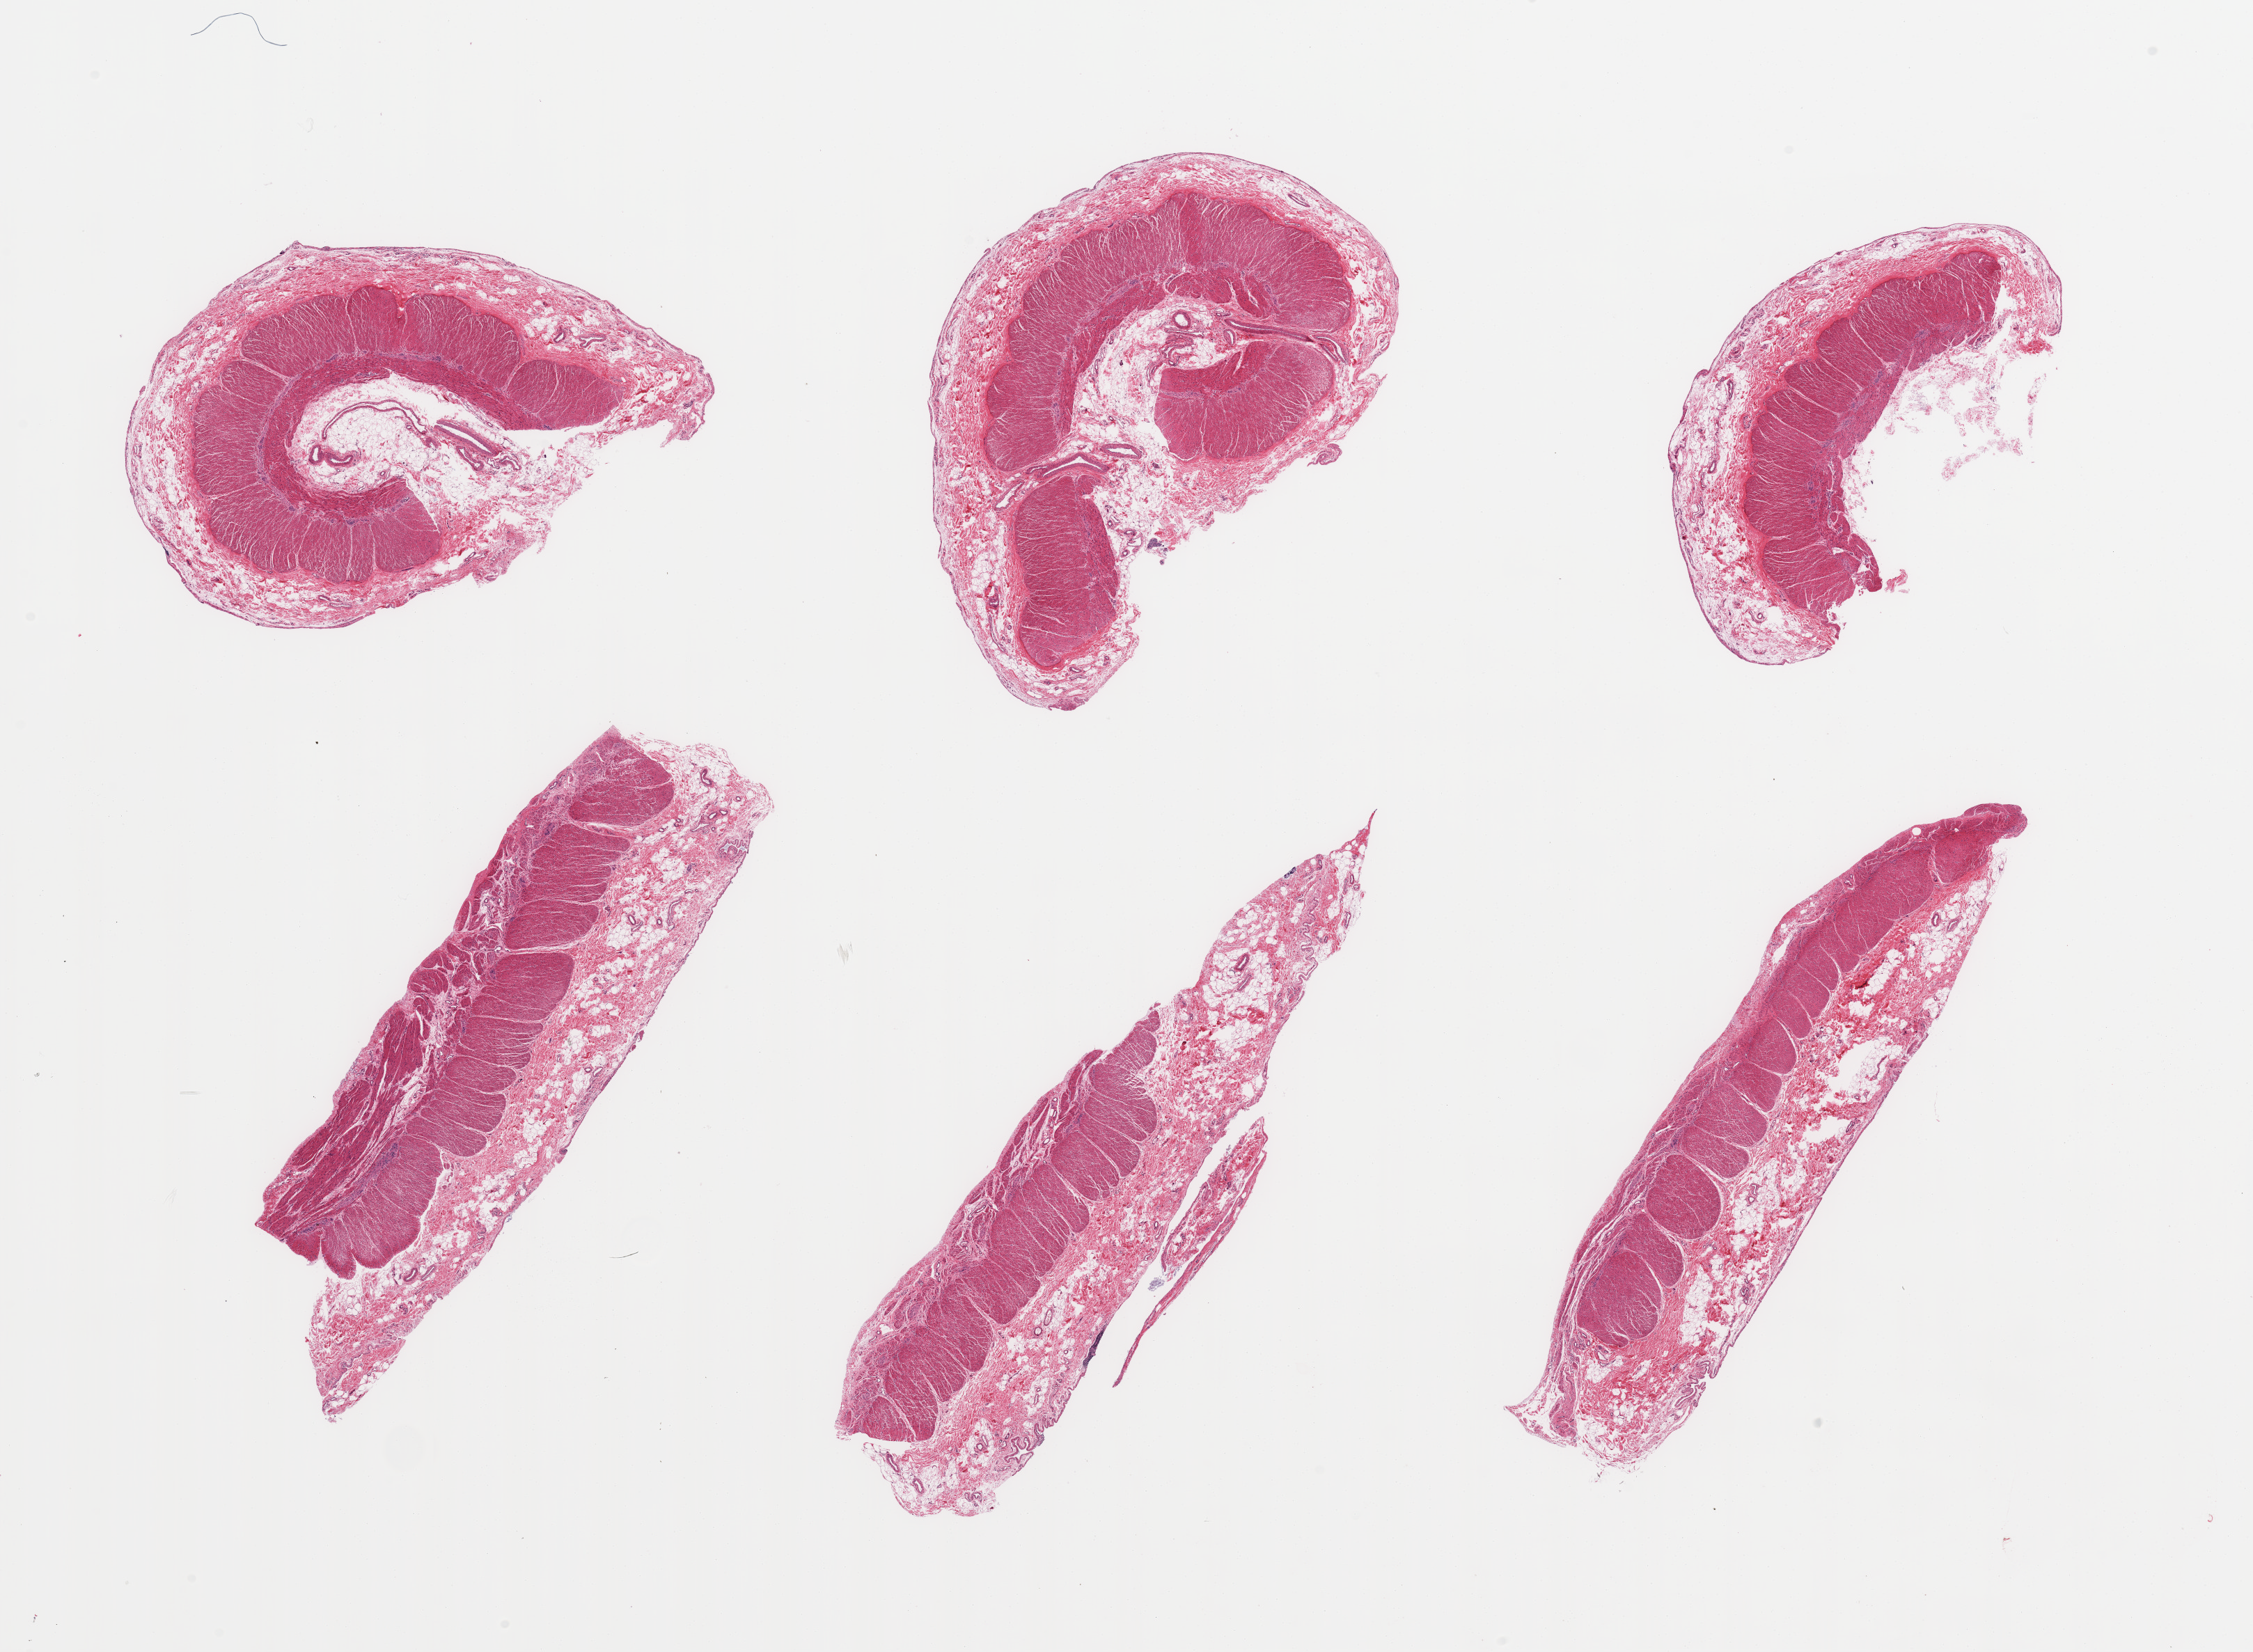
Whole-slide image, haematoxylin and eosin stain, brightfield, a low-resolution overview of the entire scanned area, about 25.6 x 18.8 mm. PAXgene-fixed paraffin-embedded (PFPE) section. Target tissue: sigmoid colon. Tissue donor sample. Male donor.
Pathologist's review note for this sample: 6 pieces; target muscularis with ~1mm attached serosa.